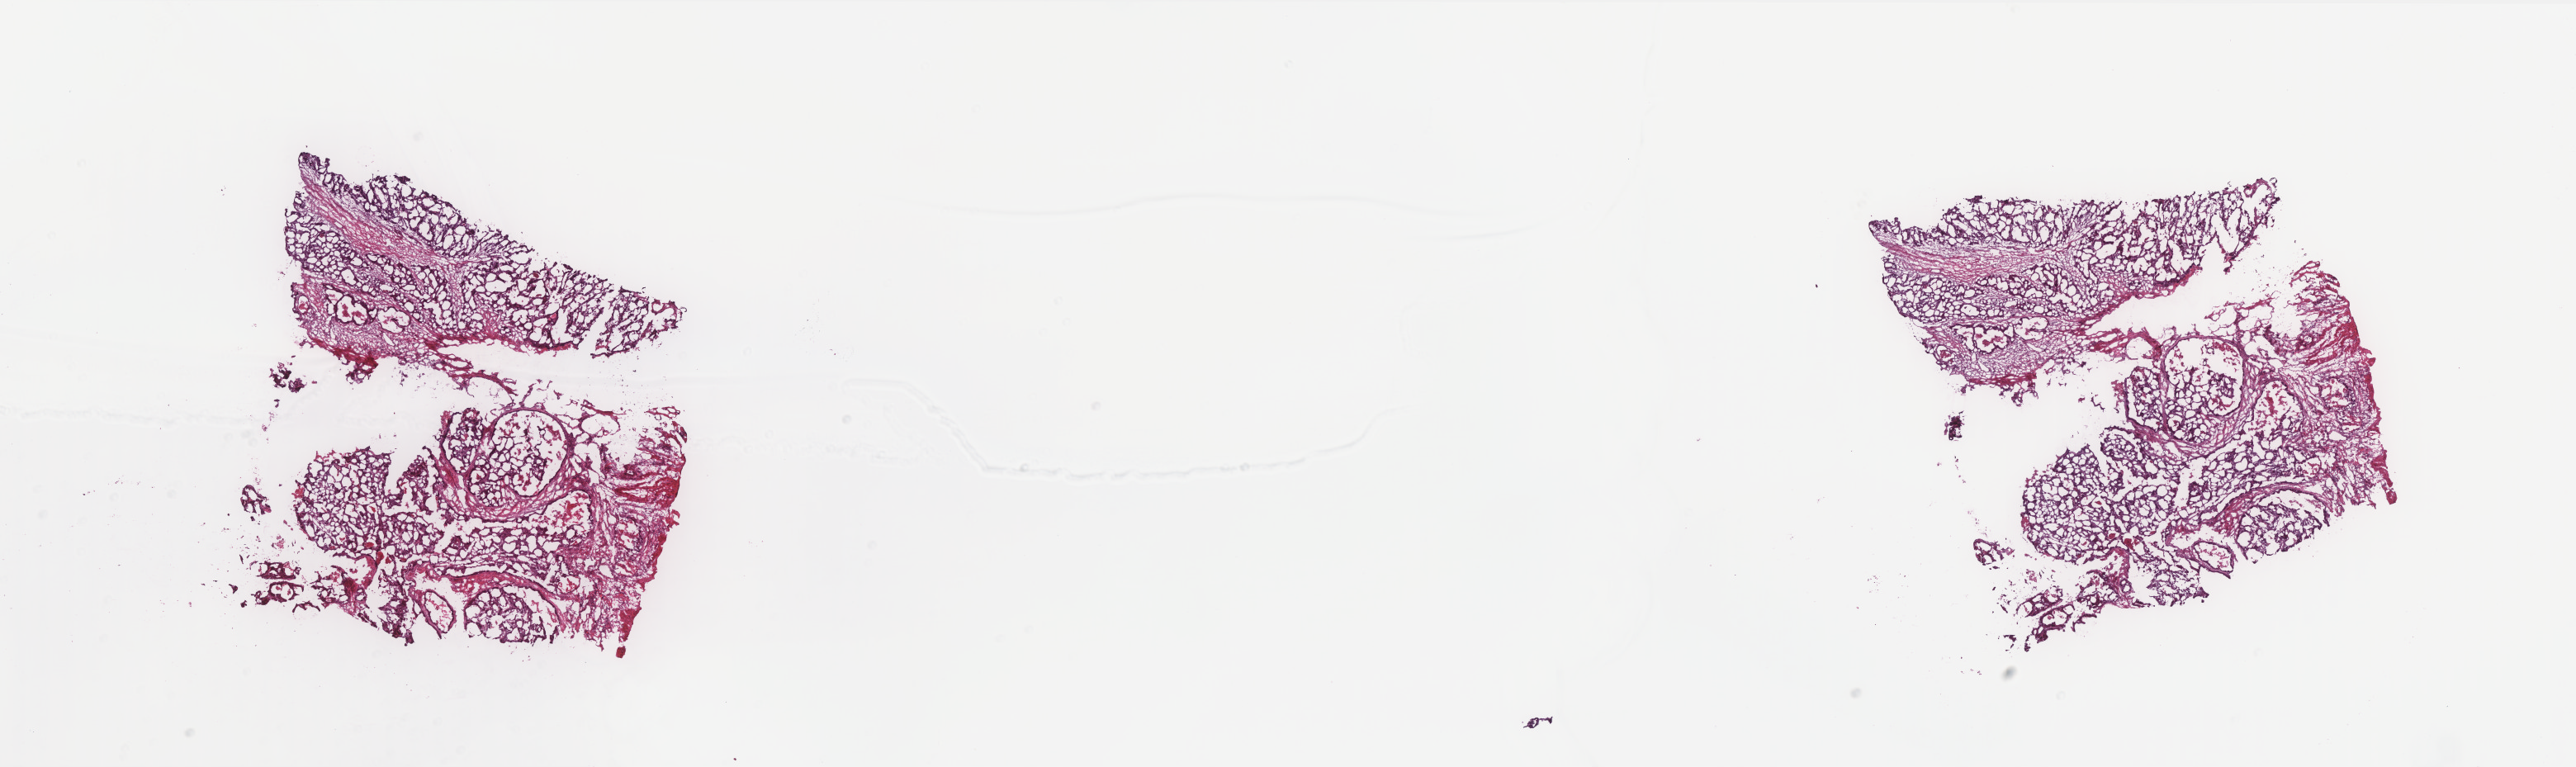
Digitized H&E-stained tissue section (whole slide) — low-resolution overview of the scanned area, about 25.0 x 7.4 mm (acquisition: 40x scan), frozen section from the top of the tissue portion, primary tumour sample from the colon. Female patient; age at initial diagnosis 50 years. Slide review estimates, as recorded: tumour cells 90%, tumour nuclei 90%, normal cells 0%, stromal cells 0%, necrosis 10%. Infiltration values recorded for this section: lymphocyte infiltration 0%, monocyte infiltration 0%, neutrophil infiltration 0%.
Lymph nodes positive (case pathology): 1 of 15 examined. Pathologic diagnosis: Adenocarcinoma, NOS (ascending colon).